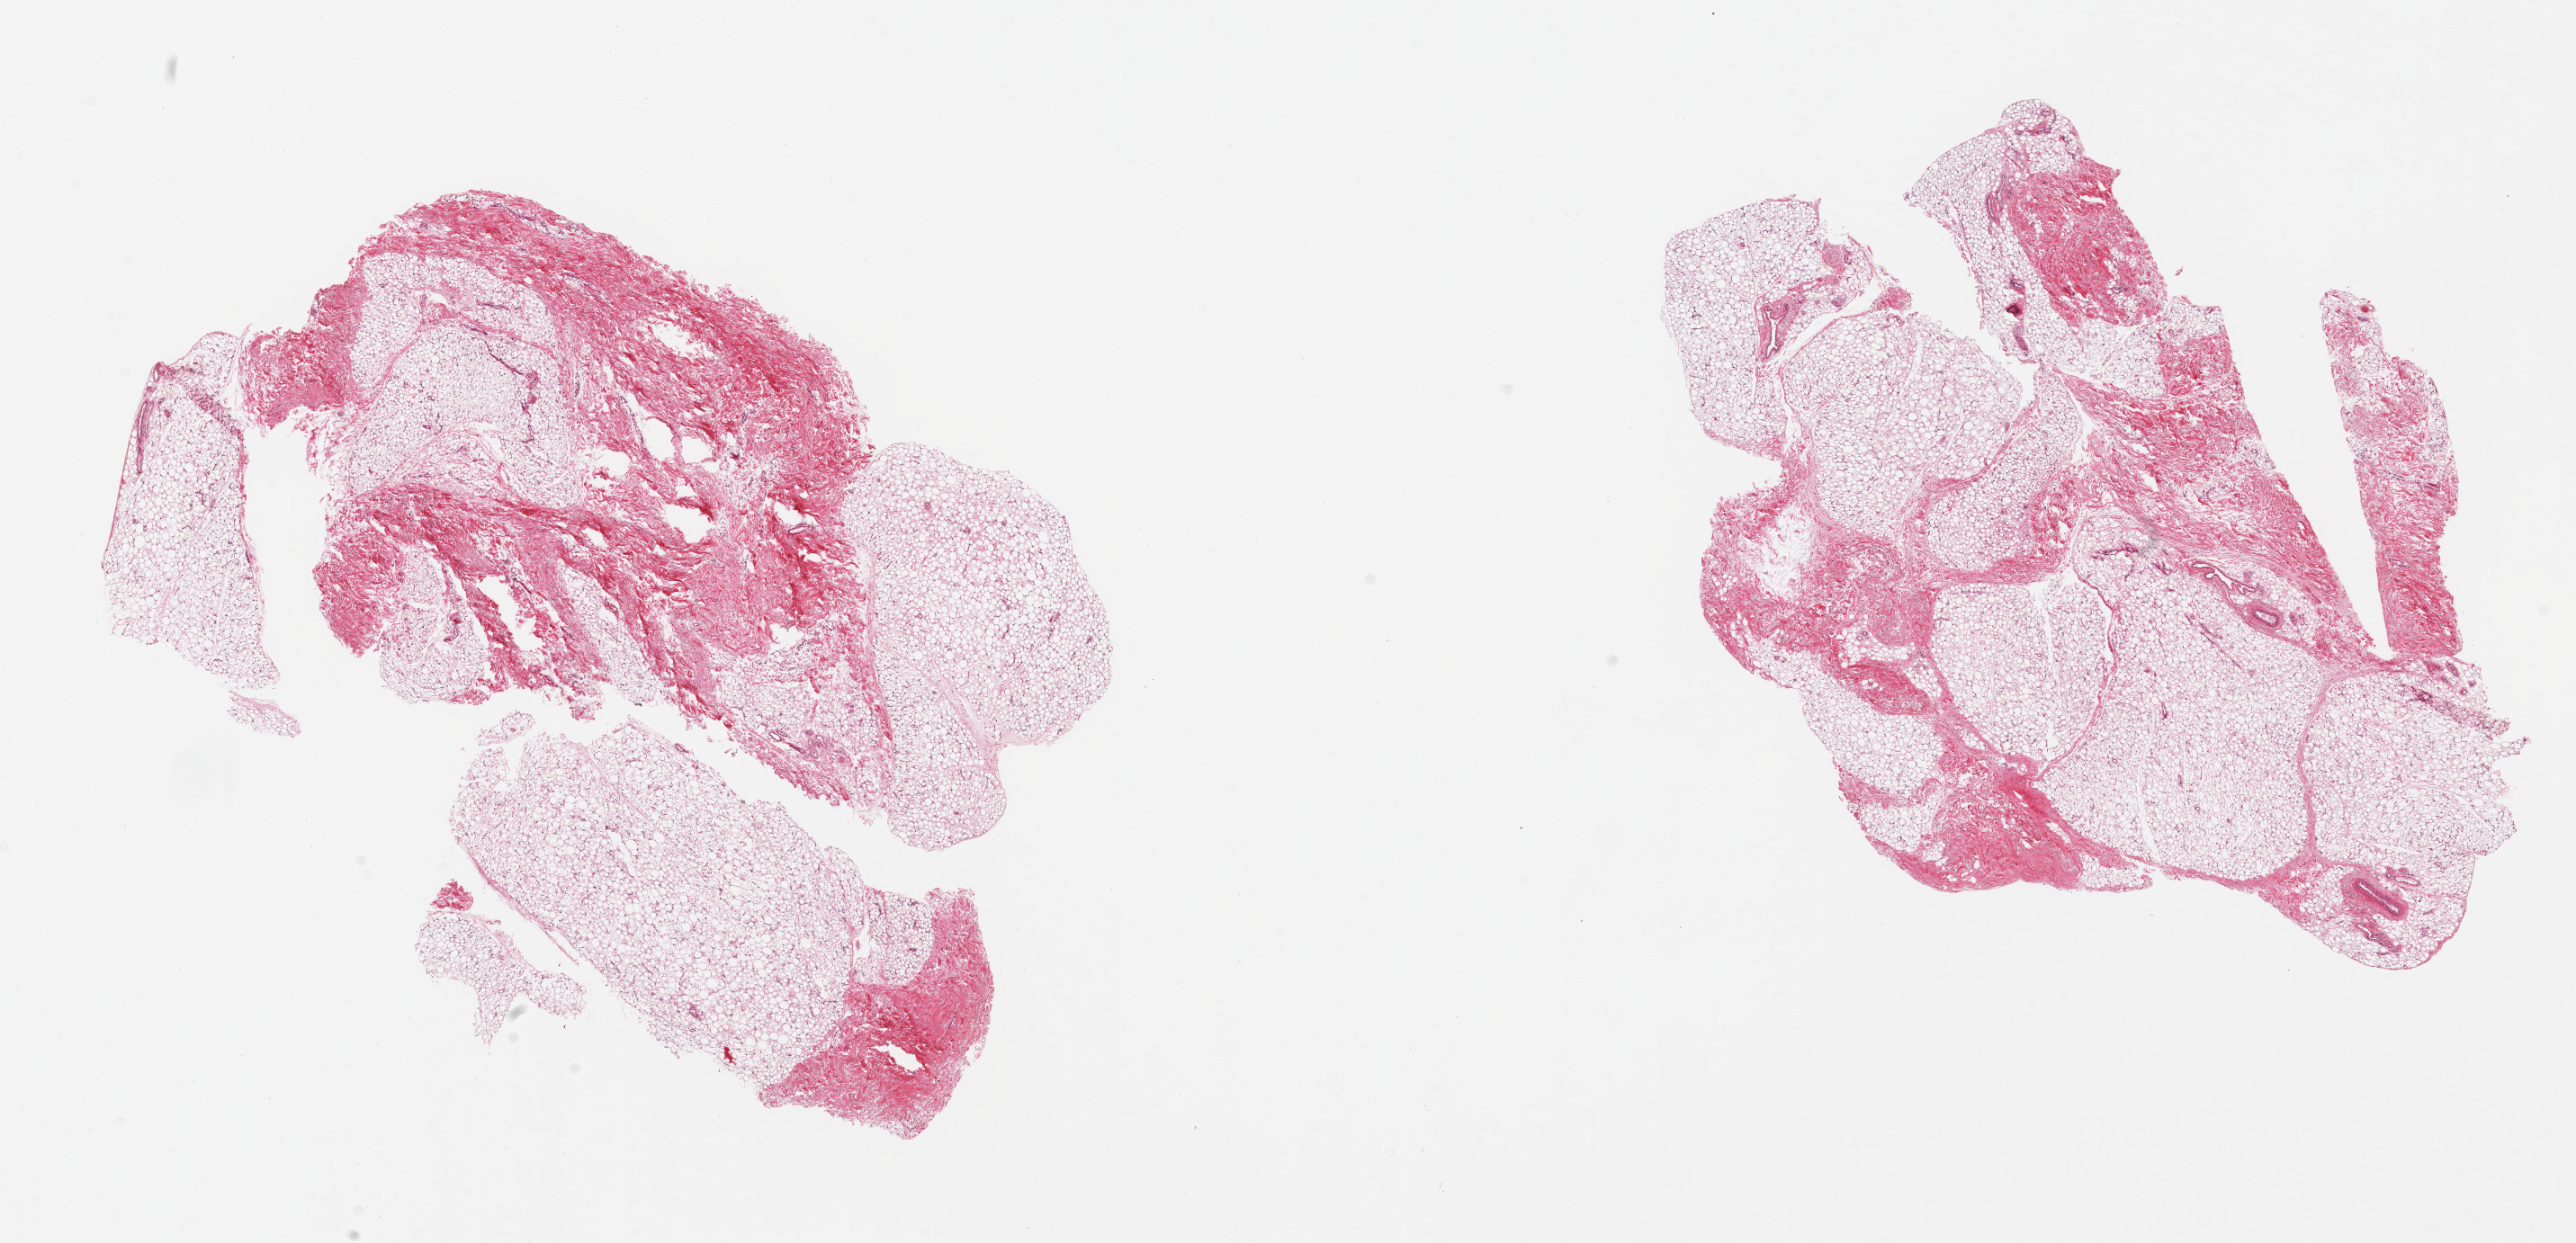
Hematoxylin and eosin (H&E) whole-slide image, low-resolution overview of the scanned area, about 22.6 x 10.9 mm (from a 20x scan). PAXgene-fixed, paraffin-embedded tissue. Target tissue: breast. Donor tissue sample.
Review note (as recorded): 2 pieces; fibroadipose tissue with no ducts.